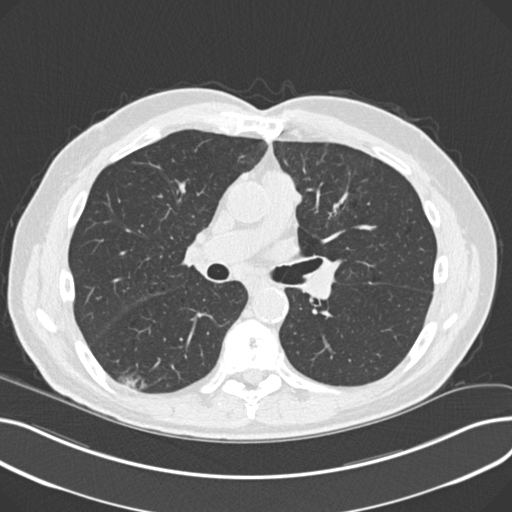
Low-dose screening chest CT, one axial slice. Position 124 of 230 along the scan axis. 120 kVp. Lung window (W 1500 / L -600 HU). 2 mm slice thickness. 512 × 512 image matrix, field of view 372 × 372 mm.
Structures marked on this image (expert manual segmentation):
- lesion 1 (nodule, lower lobe of right lung): box from (x=118, y=372) to (x=148, y=390) px